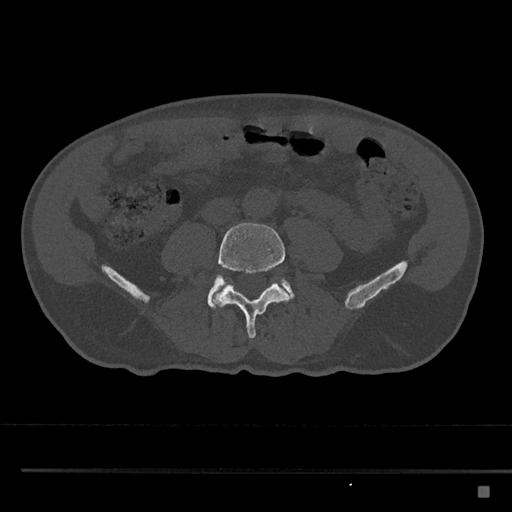
CT including the spine, one axial slice. Slice 625 of 797 in the series (ordered by position). Reconstruction kernel Br40s/3. 120 kVp. Bone window (W 1800 / L 400 HU). 512 × 512 image matrix. Male patient, age 59 years. From the clinical record (not read from this slice): primary cancer: prostate.
Annotated regions visible in this slice (semi-automatic segmentation, software-assisted and operator-edited):
- L4 vertebra: bounding box (x1, y1, x2, y2) in pixels: (213, 222, 290, 339)
- L5 vertebra: (207, 275, 295, 309)